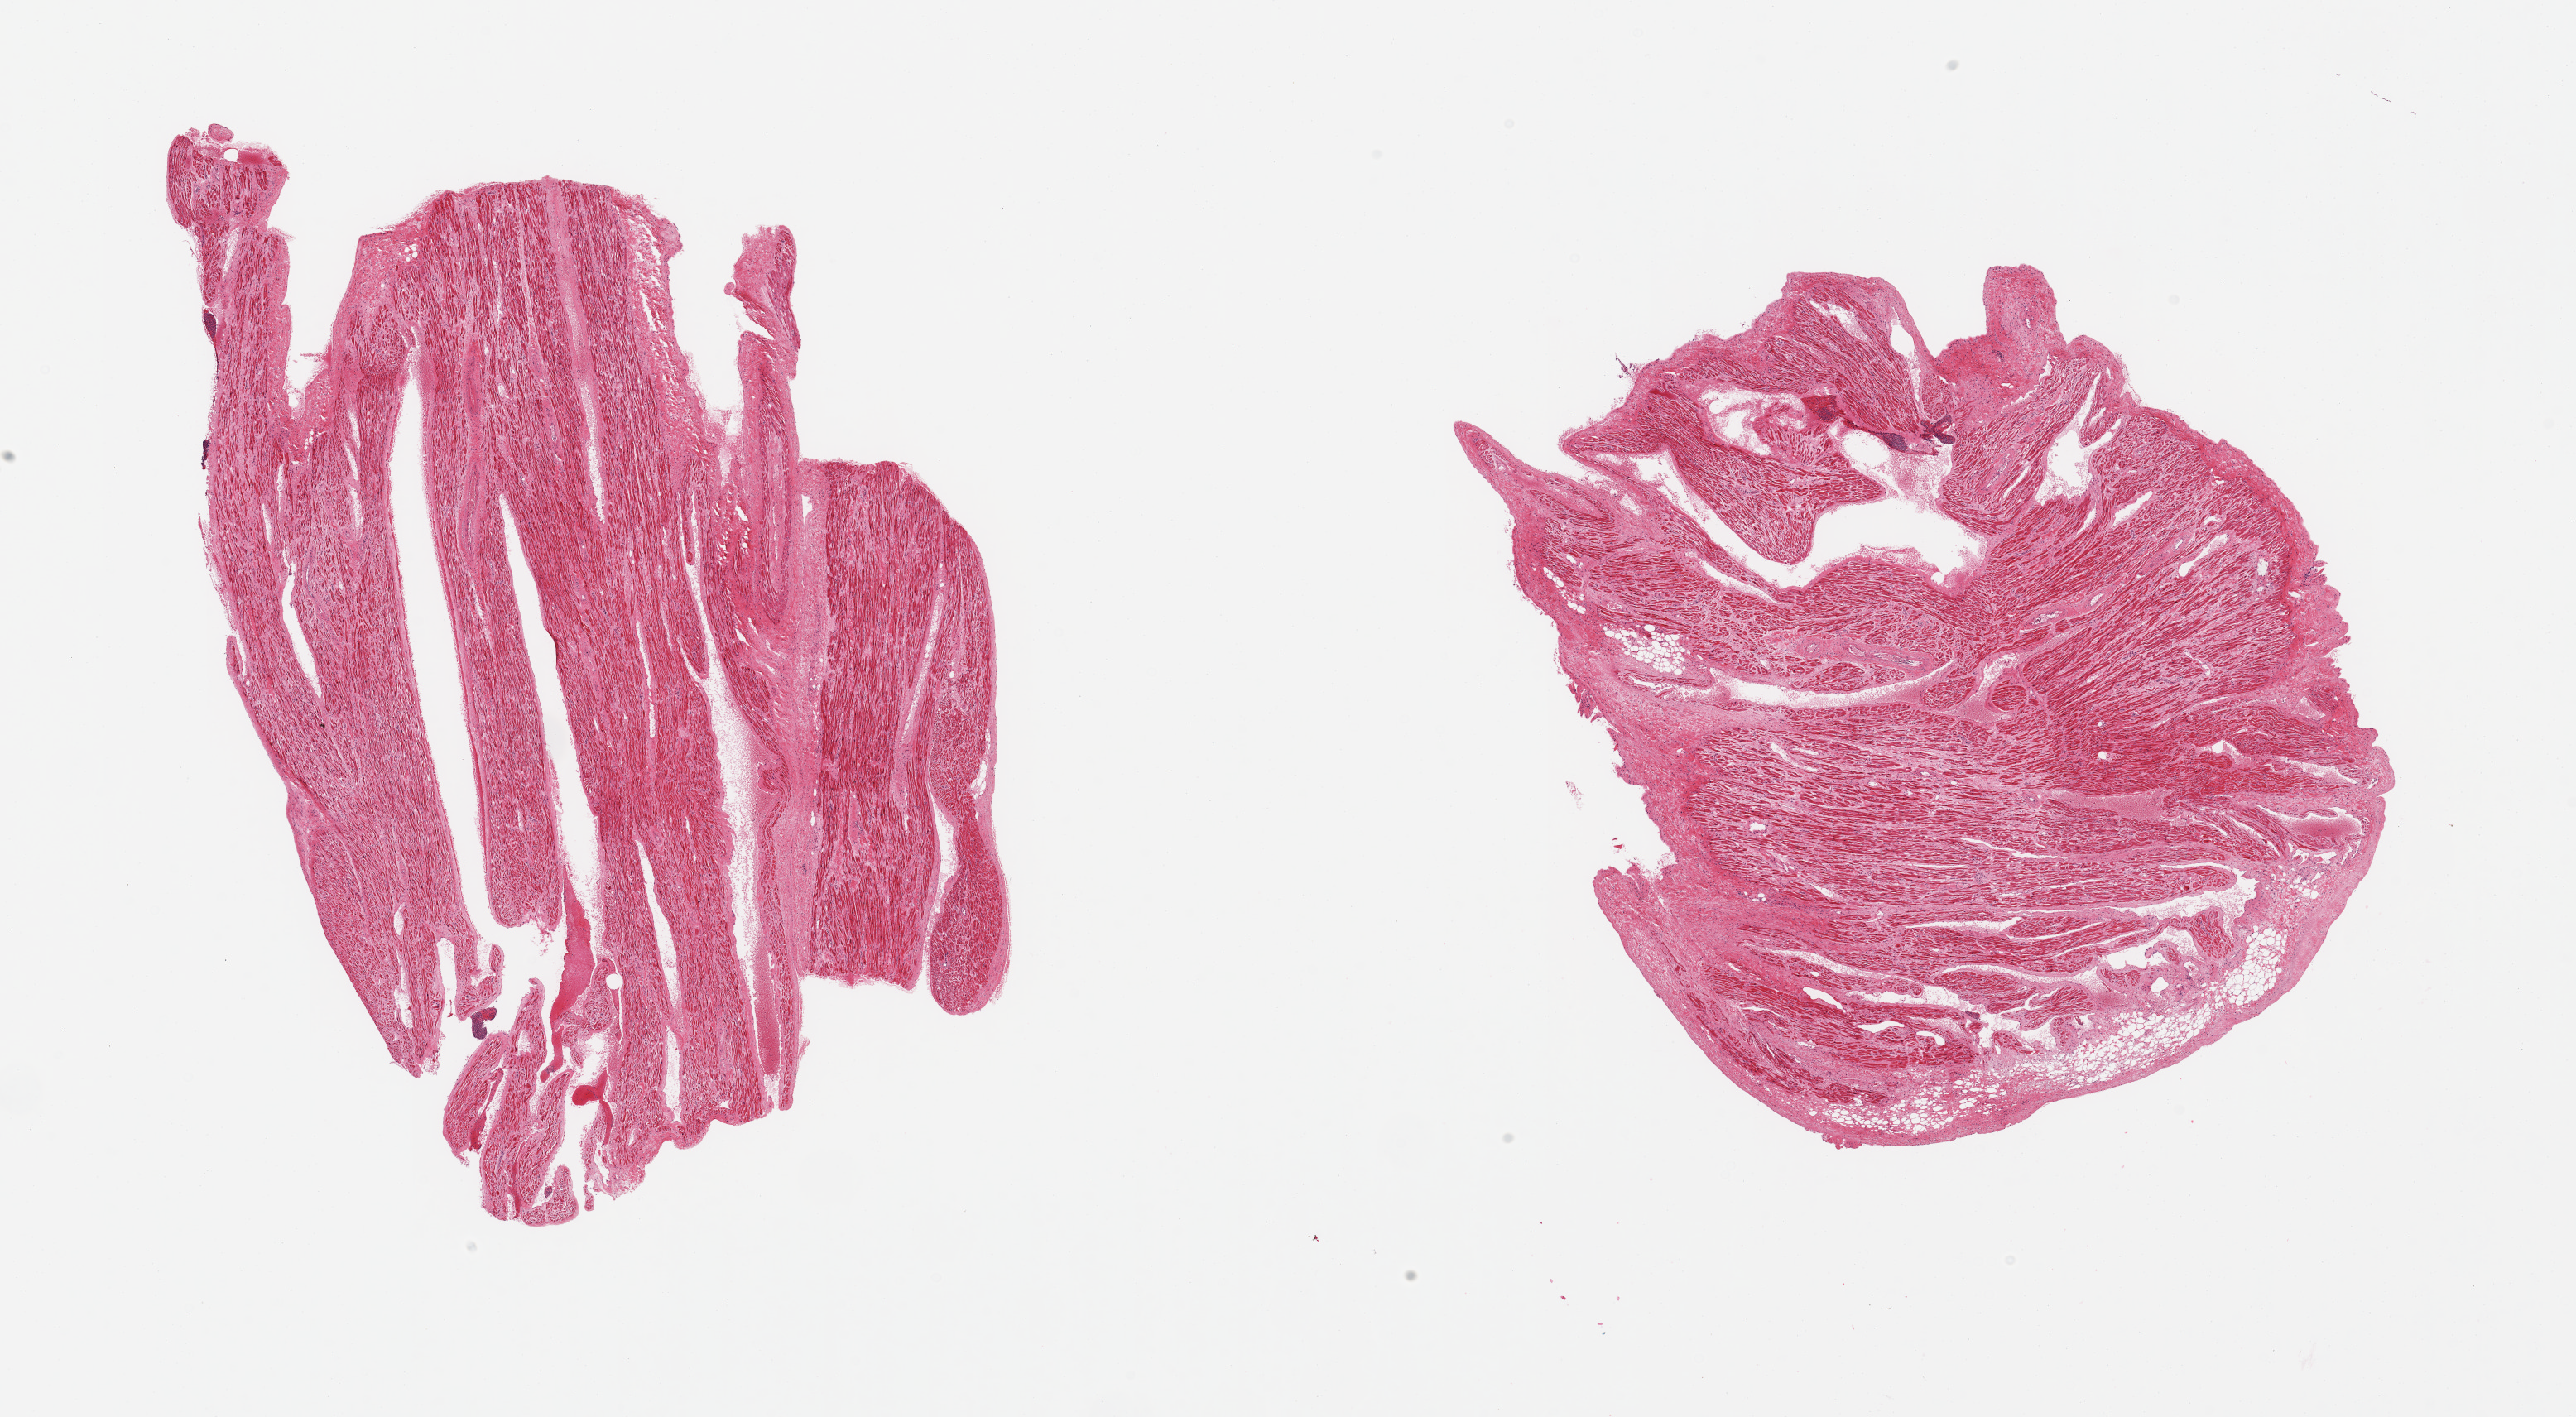
Digitized haematoxylin and eosin-stained section — low-resolution overview of the scanned area, about 24.6 x 13.5 mm; PAXgene-fixed paraffin-embedded (PFPE) section; target tissue: auricular appendage; donor tissue sample.
- reviewer comment on this tissue sample: 2 pieces; 5 & 10% internal fibrofatty content